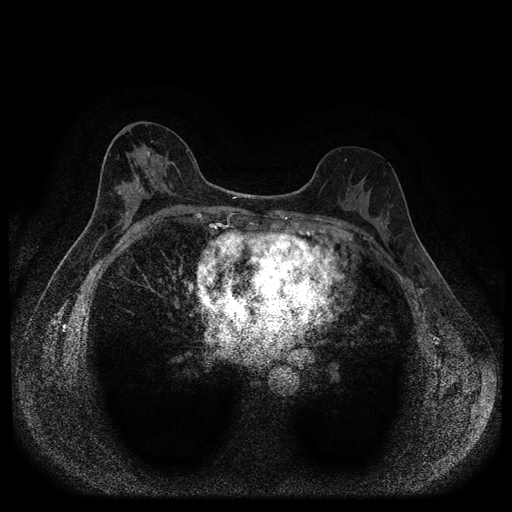
Breast MRI (dynamic contrast-enhanced, multi-phase), one axial slice; position 53 of 116 along the scan axis; dynamic contrast-enhanced series, time point 2 of 5 at this slice position (early post-contrast); 1.5 T; TE 2.7 ms, TR 5.4 ms; 2 mm slice thickness; 512 × 512 image matrix, field of view 330 × 330 mm. Female patient, age 49 years.
Annotated regions visible in this slice (semi-automatic segmentation, software-assisted and operator-edited):
- breast lesion (labelled 'tumour' in the annotation; benign lesions carry a separate 'benign' label): bounding box (x1, y1, x2, y2) in pixels: (116, 186, 122, 195)